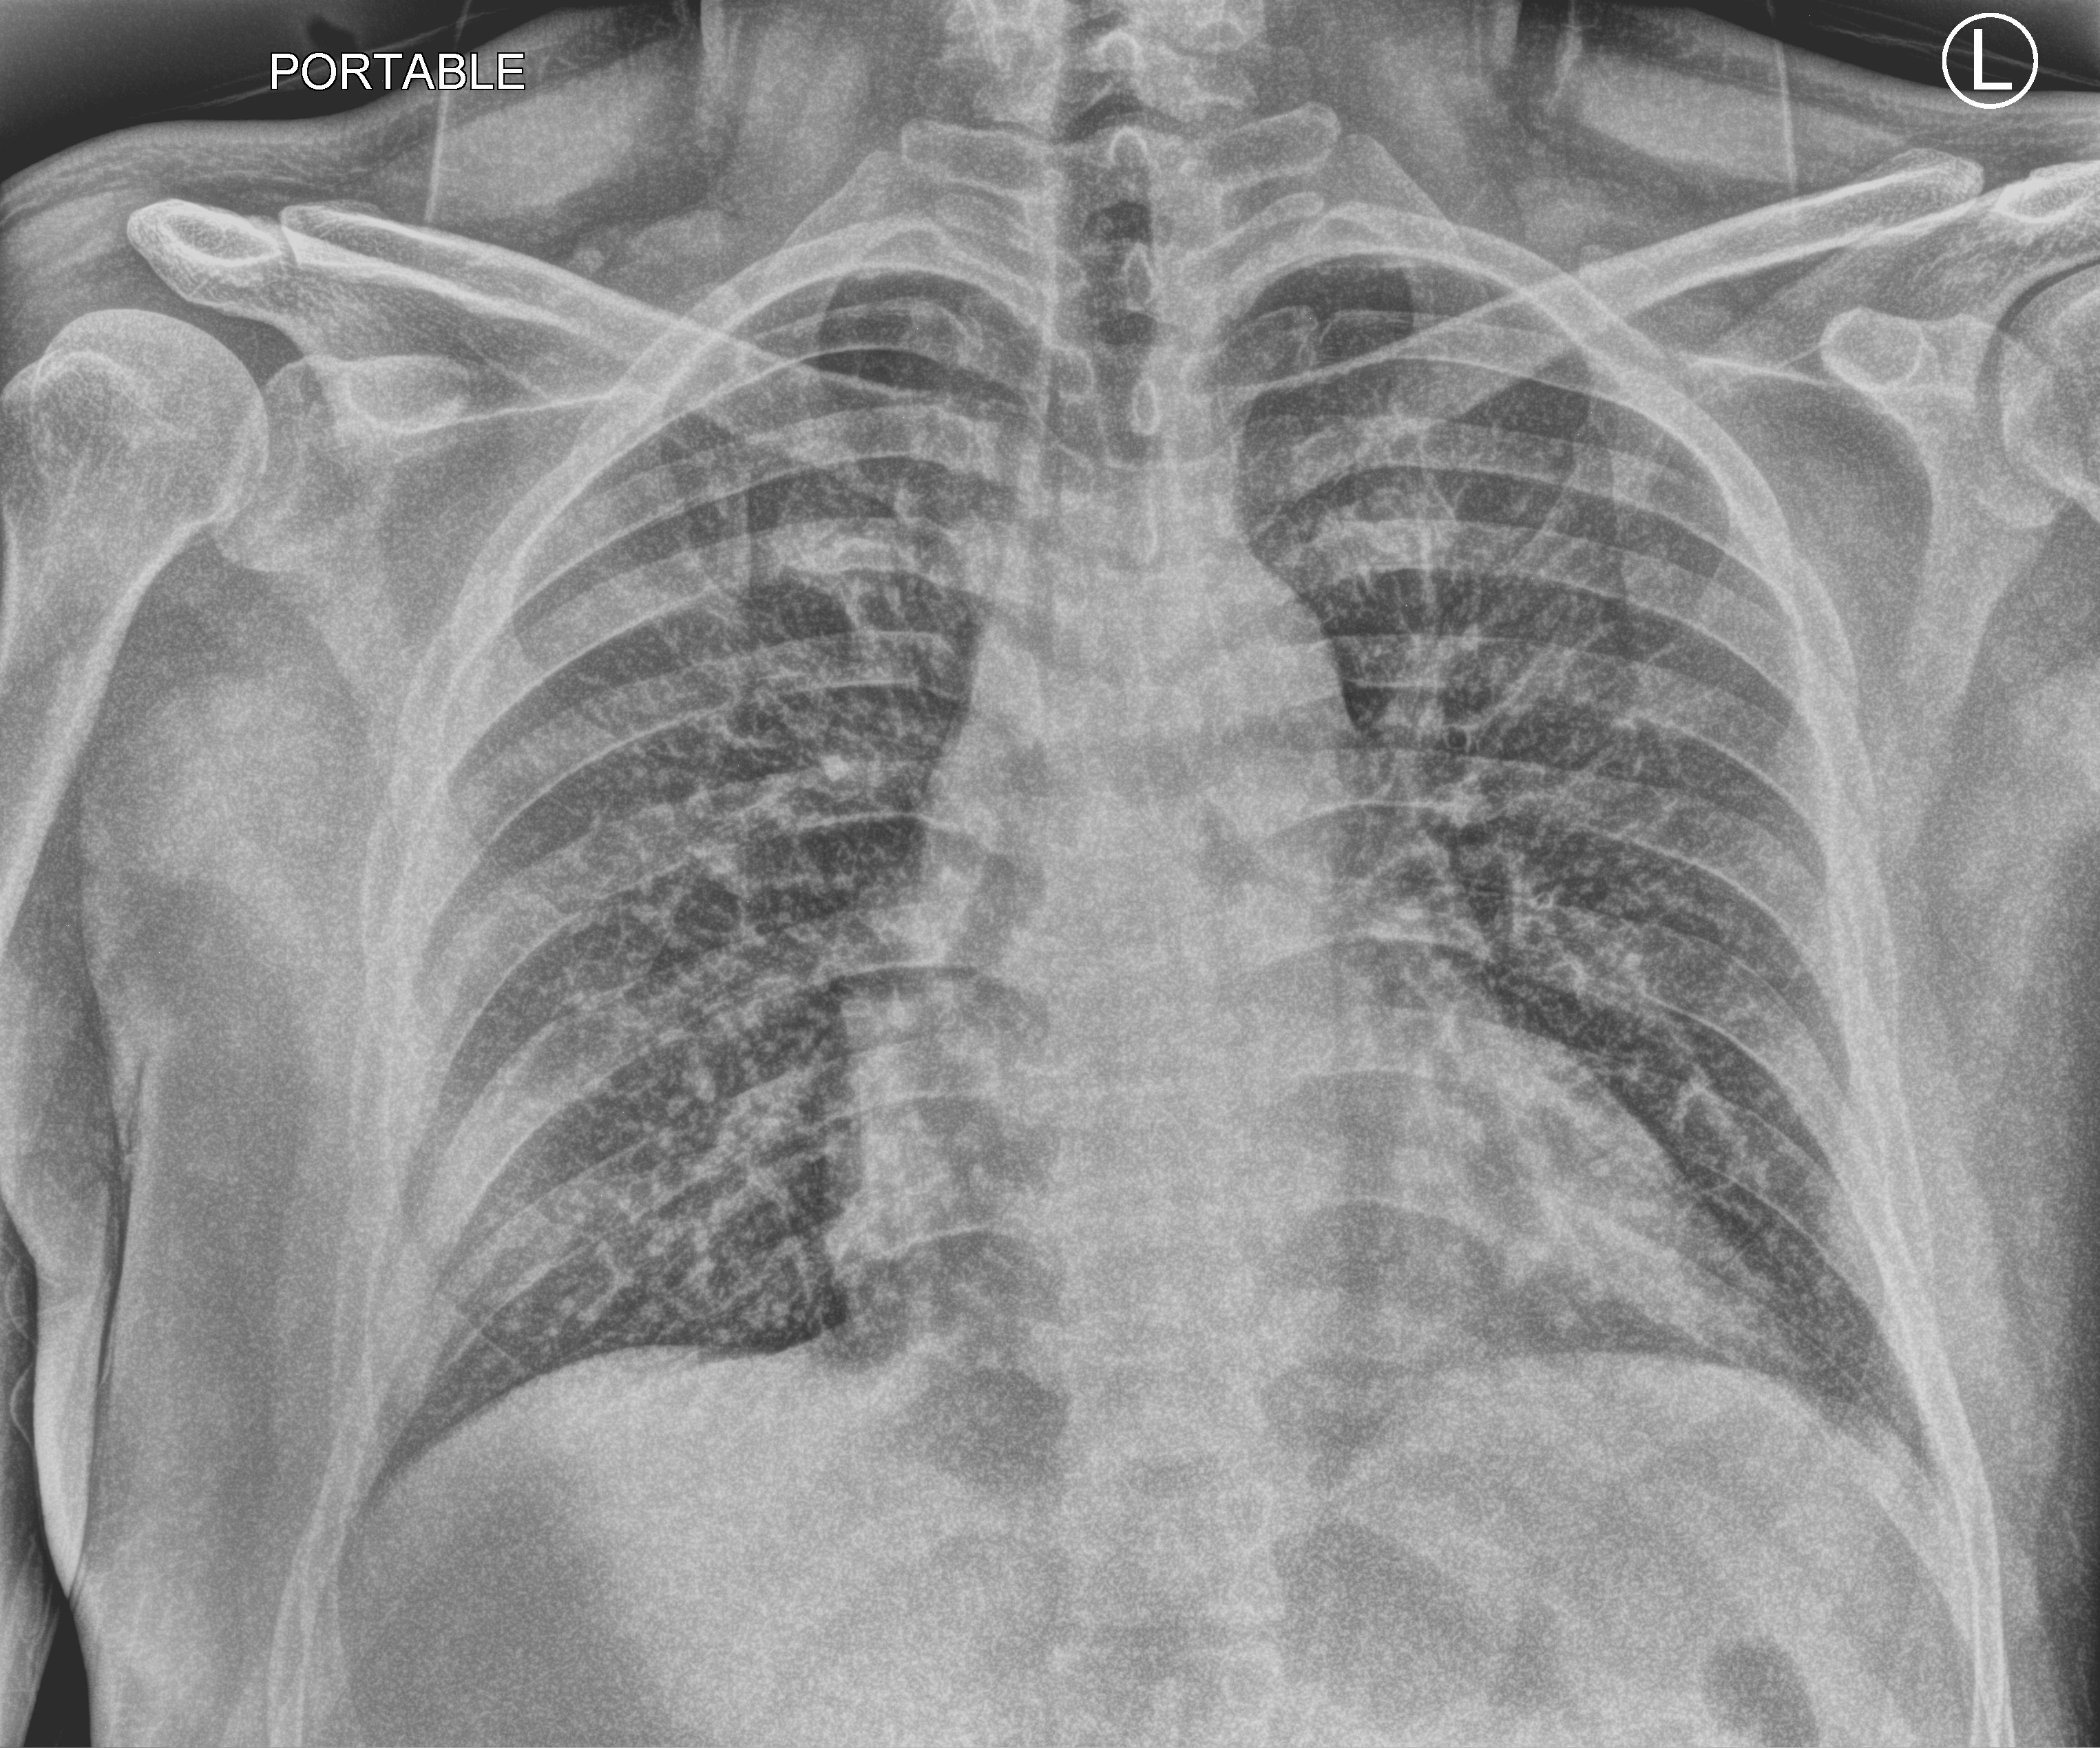
Chest X-ray (portable); anteroposterior (AP) projection. Male patient hospitalised with COVID-19, age 18–59 years.
From the hospital-stay record, not from the radiograph (when in the stay this image was taken is not recorded): hypertension (admission record): no; mechanically ventilated during this hospital stay: no.